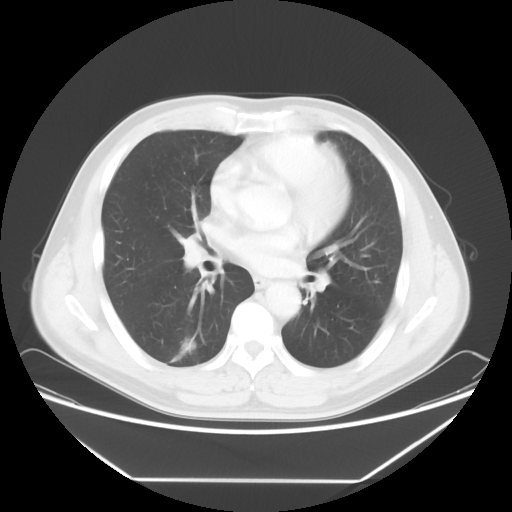
Chest CT, one axial slice. Slice 33 of 65 in the series (ordered by position). 120 kVp. Lung window (W 1500 / L -600 HU). 5 mm slice thickness. 512 × 512 image matrix, field of view 418 × 418 mm. Patient: male, 50 years. Case-level facts recorded for this patient, not image findings: clinical TNM (as recorded): T1c N0 M0; histopathological grade: G3.
Outlined on this slice (bounding box drawn by a radiologist):
- lung tumour (recorded histology: adenocarcinoma): bounding box <165,333,198,364> (left, top, right, bottom; pixels)